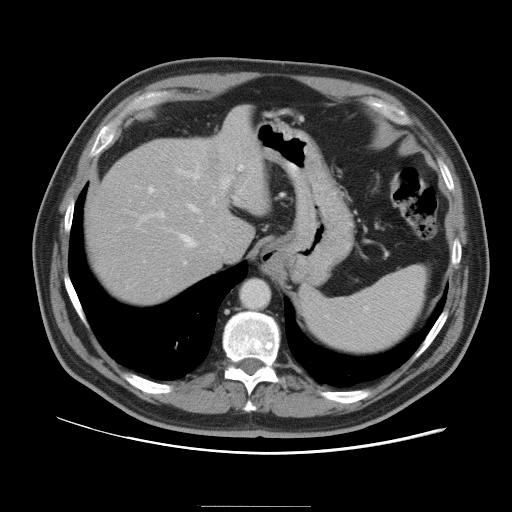
Contrast-enhanced abdominal CT, one axial slice; position 77 of 105 along the scan axis; intravenous contrast given; soft-tissue window (W 400 / L 40 HU); 5 mm slice thickness; 512 × 512 image matrix. Male patient, age 64 years. Case-level facts recorded for this patient, not image findings: diagnosis: colorectal cancer liver metastases, imaged before liver resection; multiple liver metastases: yes; largest metastasis: 3 cm; disease in both lobes: yes.
Structures marked on this image (expert manual segmentation):
- hepatic veins: box from (x=180, y=204) to (x=200, y=247) px
- liver: (x=88, y=108)–(x=267, y=304)
- planned liver remnant (the part of the liver to remain after resection): (x=88, y=146)–(x=232, y=304)
- portal vein (with intrahepatic branches): (x=138, y=162)–(x=243, y=264)
- liver metastasis: (x=209, y=150)–(x=219, y=171)